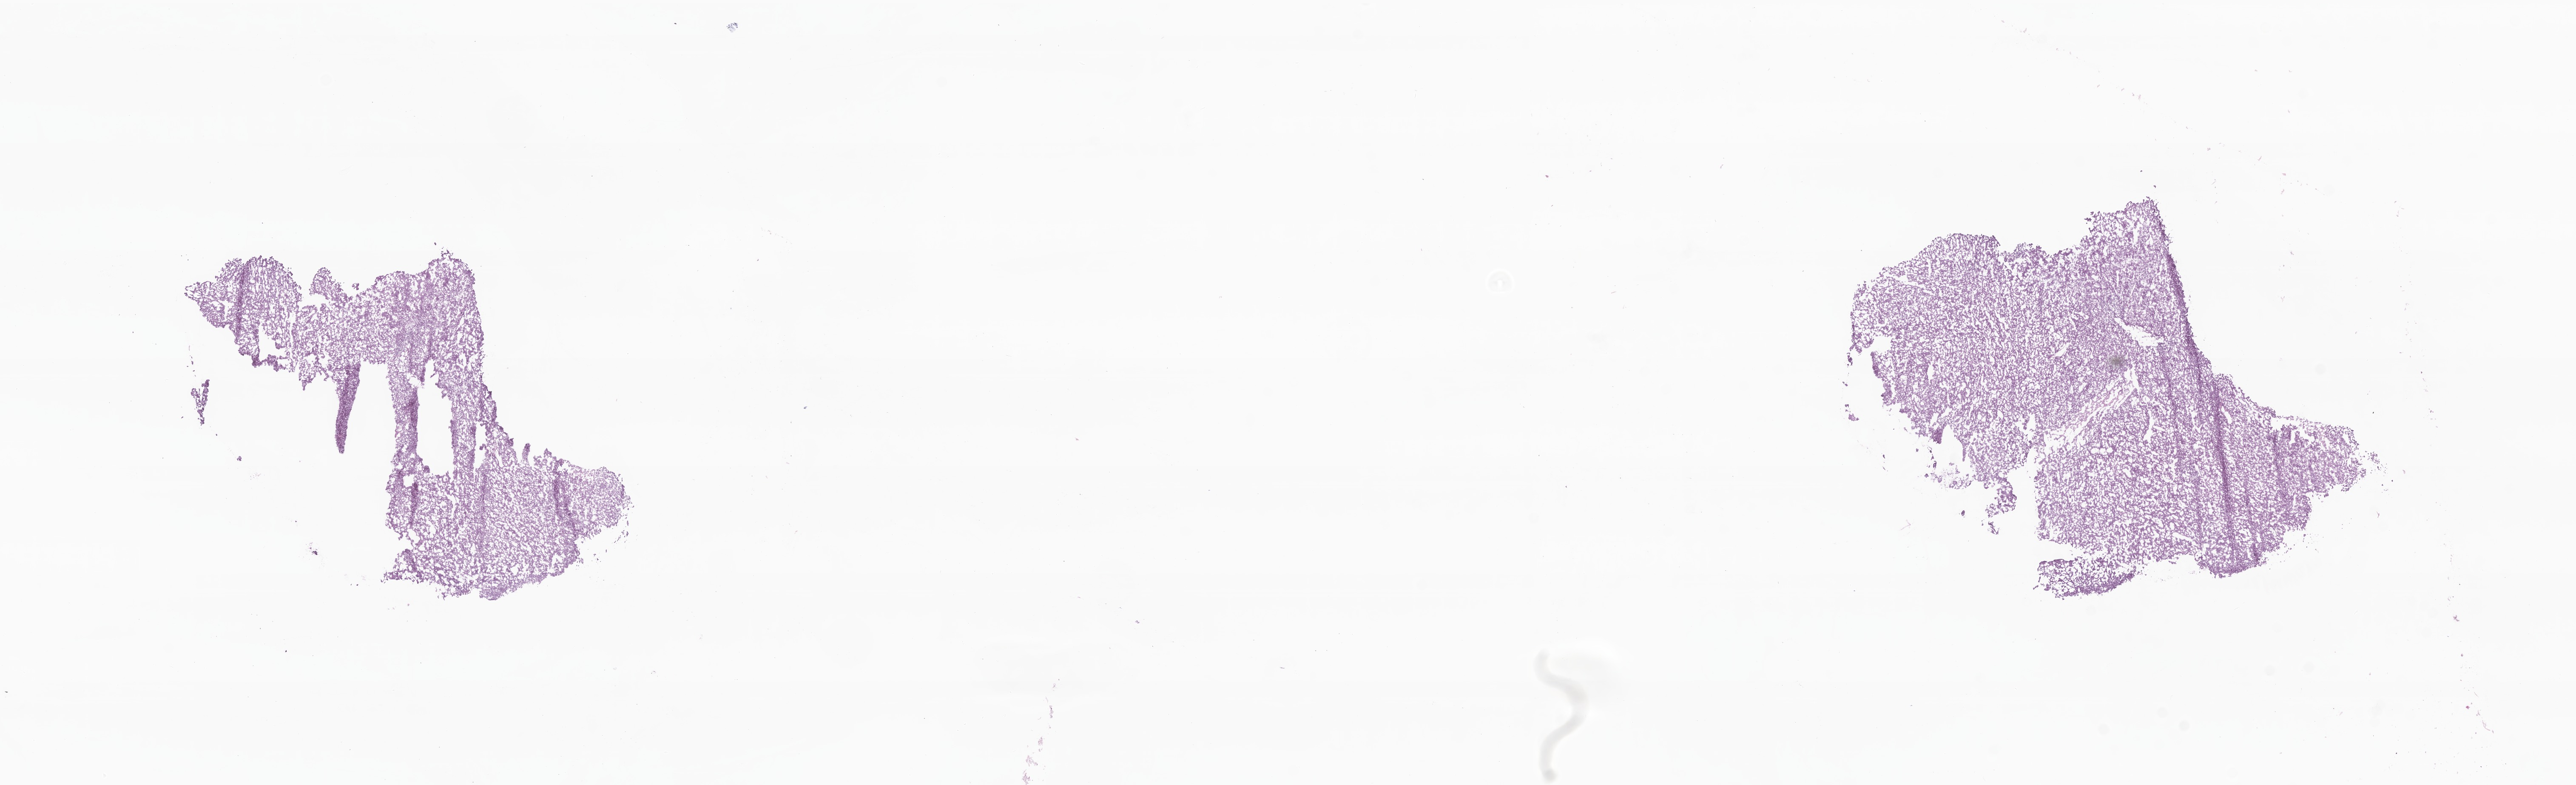
Haematoxylin and eosin whole-slide image, shown as a low-resolution overview of the whole scanned area (about 25.5 x 7.8 mm), frozen section (tissue freezing medium), specimen: primary tumor, site: liver. Male patient; age at initial diagnosis 86 years. Tumor grade: G3 (poorly differentiated). Composition of this section per pathologist review: tumor cells 90%, tumor nuclei 90%, stromal cells 10%, necrosis 0%, normal cells 0%. Infiltration values recorded for this section: lymphocyte infiltration 0%, monocyte infiltration 0%, neutrophil infiltration 0%.
AJCC pathologic stage: Stage IIIB. Histologic diagnosis: Hepatocellular carcinoma, NOS.